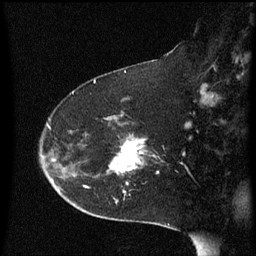
Breast MRI (dynamic contrast-enhanced), one sagittal slice. Slice 39 of 60 in the series (ordered by position). Dynamic contrast-enhanced series, image 2 of 3 at this slice position (ordered by acquisition). 1.5 T. TE 4.2 ms, TR 8.4 ms. 2 mm slice thickness. 256 × 256 image matrix, field of view 200 × 200 mm. Patient: female, 54 years. Case-level facts recorded for this patient, not image findings: setting: breast cancer imaged before/during neoadjuvant chemotherapy; receptor status: HR-positive, HER2-negative.
Annotated regions visible in this slice (semi-automatic segmentation, software-assisted and operator-edited):
- analysis volume of interest (the breast-tissue region the enhancement analysis was run in; not a lesion): bounding box <95,120,160,179> (left, top, right, bottom; pixels)
- tumour enhancement mask (voxels above the 70 % enhancement threshold inside the analysis volume of interest): <112,142,144,175>